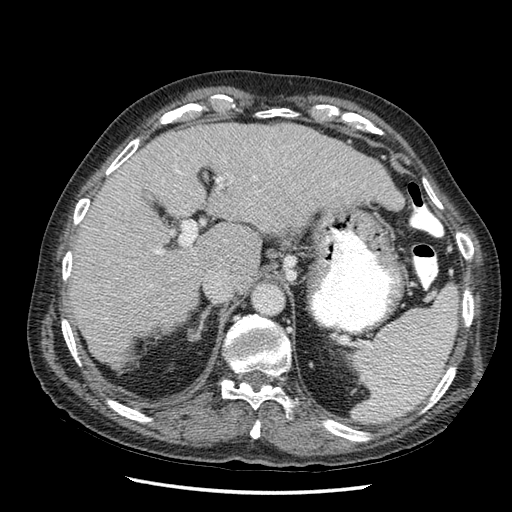
Contrast-enhanced abdominal CT (liver protocol), one axial slice; position 35 of 67 along the scan axis; 120 kVp; soft-tissue window (W 400 / L 40 HU); 512 × 512 image matrix, field of view 360 × 360 mm. Case-level facts recorded for this patient, not image findings: diagnosis: hepatocellular carcinoma (patient treated with transarterial chemoembolisation; whether this scan precedes or follows treatment is not stated here); TNM stage (as recorded): Stage-I; Child-Pugh class: A; tumour nodularity: uninodular.
Outlined on this slice (semi-automatic segmentation, software-assisted and operator-edited):
- liver parenchyma outside the tumour (the mass and vessels are separate outlines, so this box may not span the whole liver): box from (x=67, y=122) to (x=402, y=374) px
- liver vessels: (x=68, y=170)–(x=231, y=280)